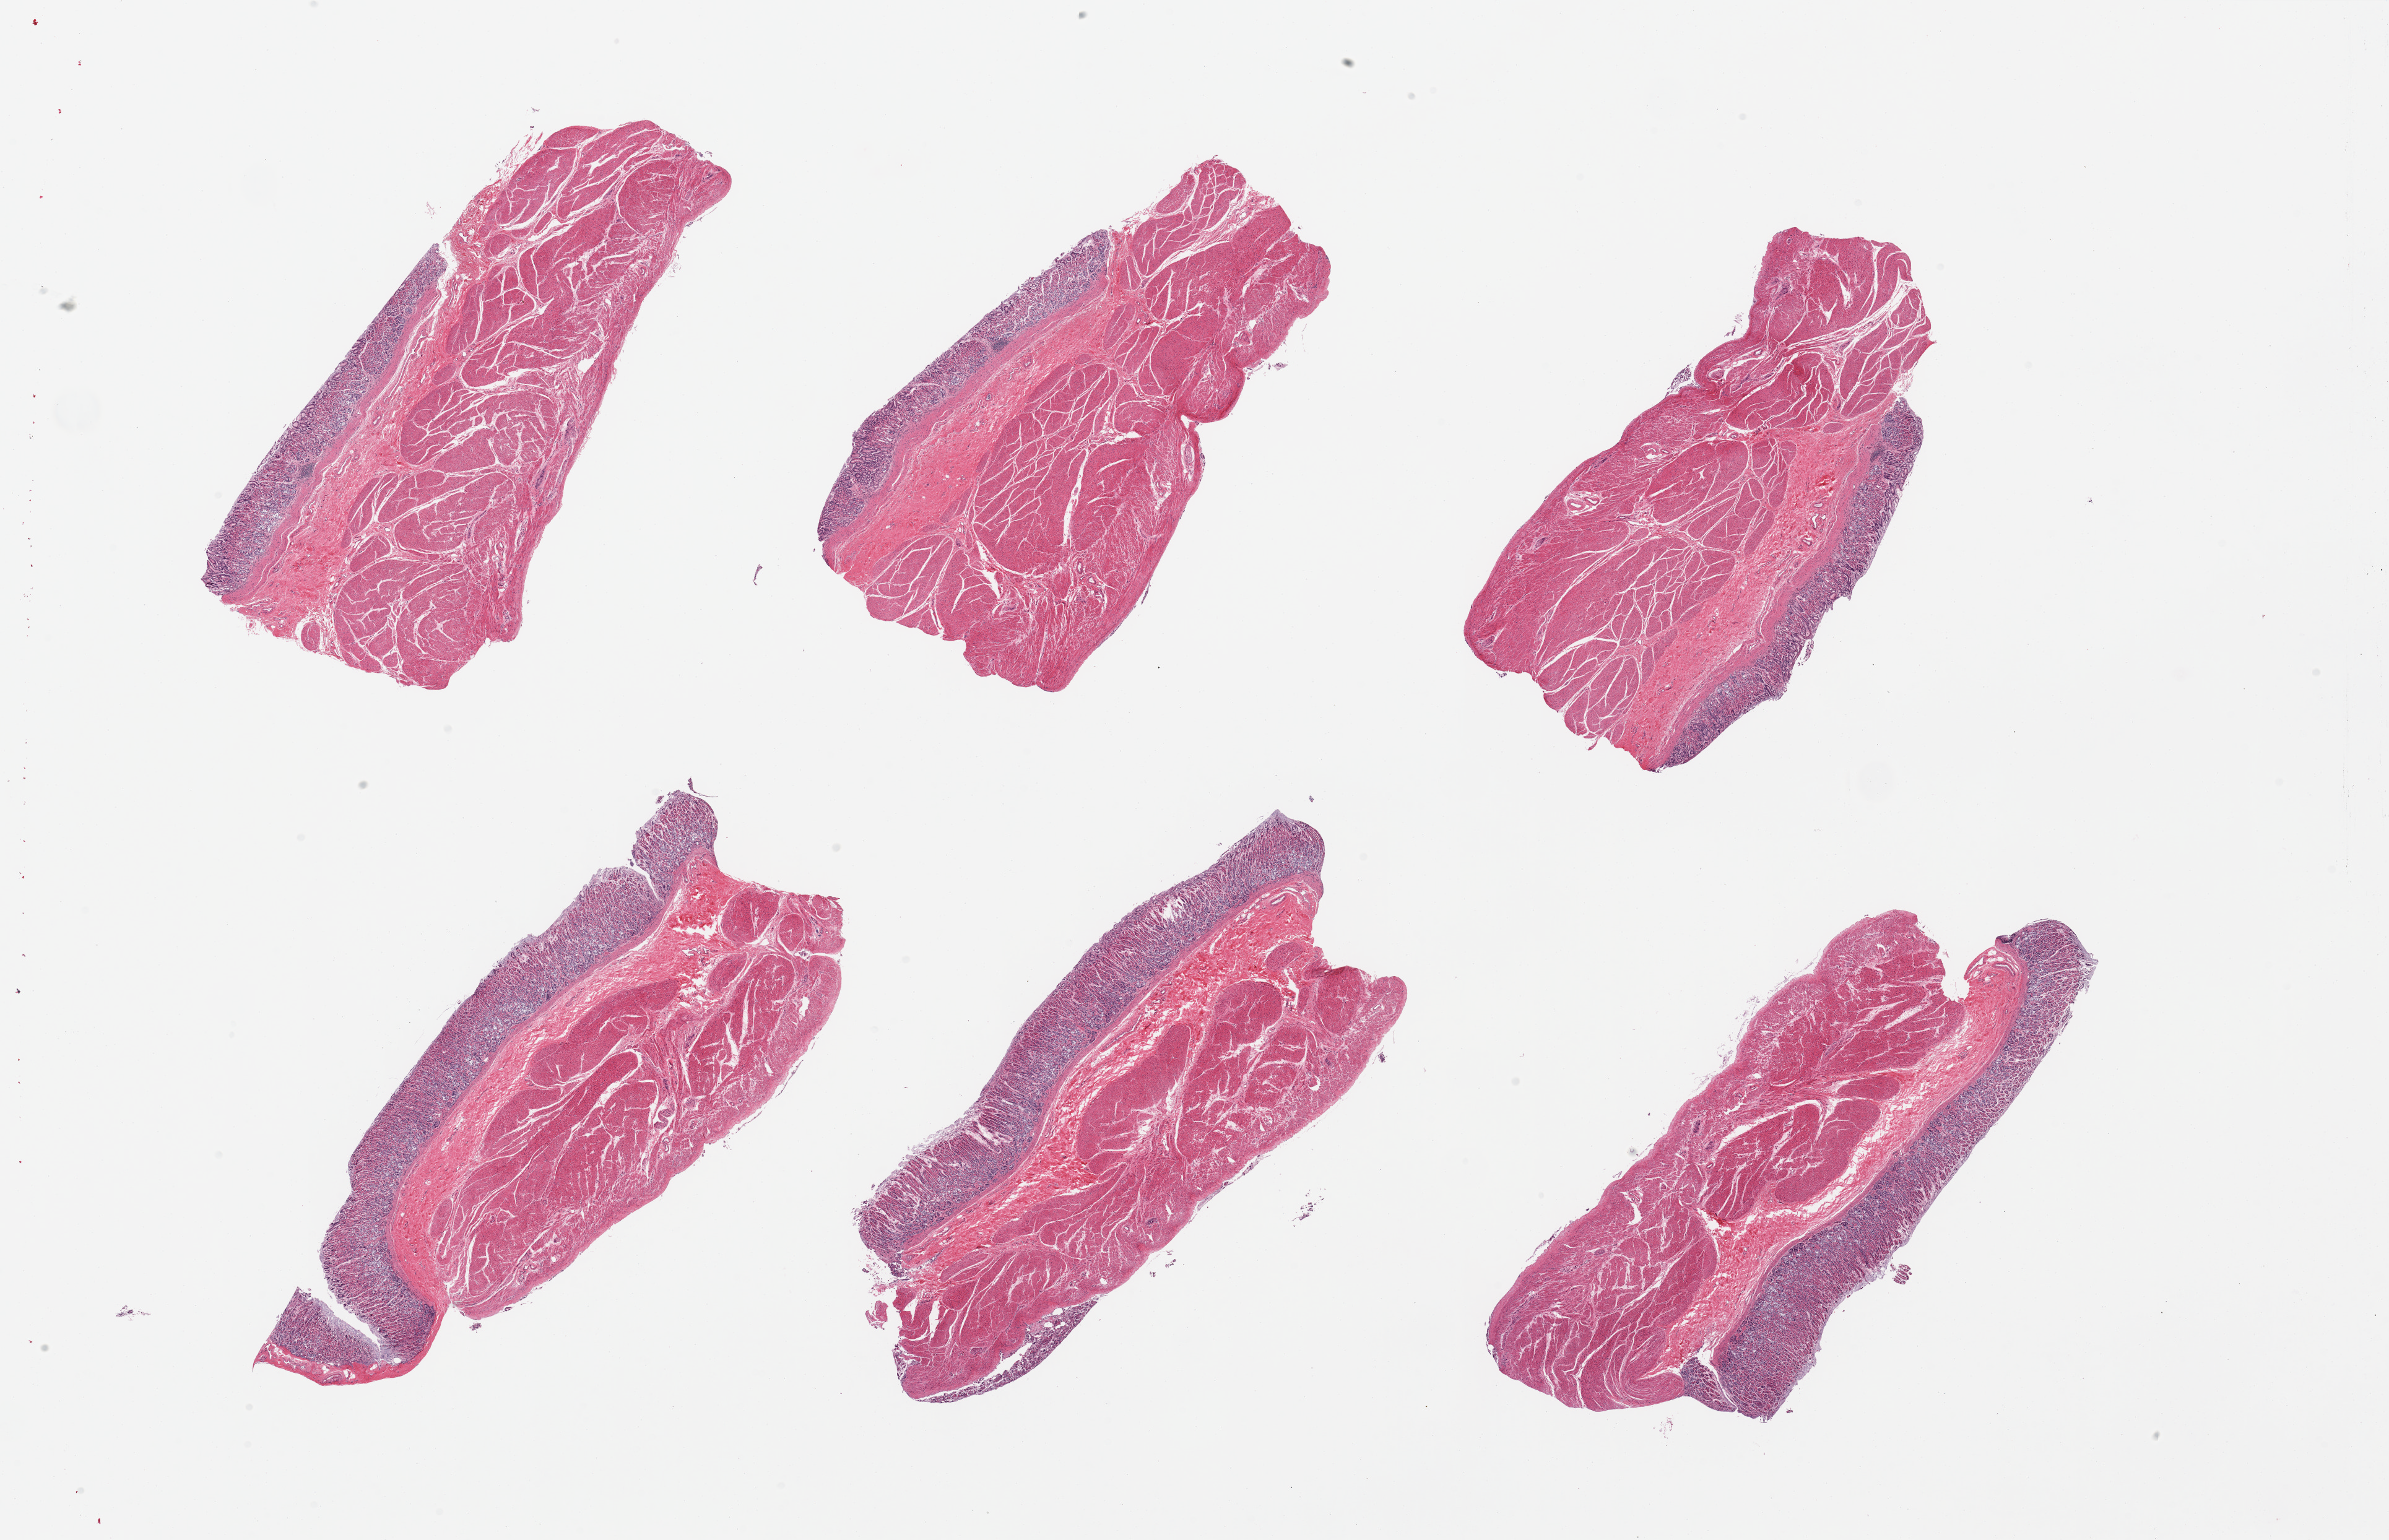
Whole-slide image, hematoxylin and eosin (H&E) stain — shown as a low-resolution overview of the whole scanned area (about 30.5 x 19.7 mm); PAXgene-fixed paraffin-embedded (PFPE) section; sampled site (target tissue): stomach; tissue donor sample. Donor: female.
Review note (as recorded): 6 pieces; full thickness sections, well preserved.